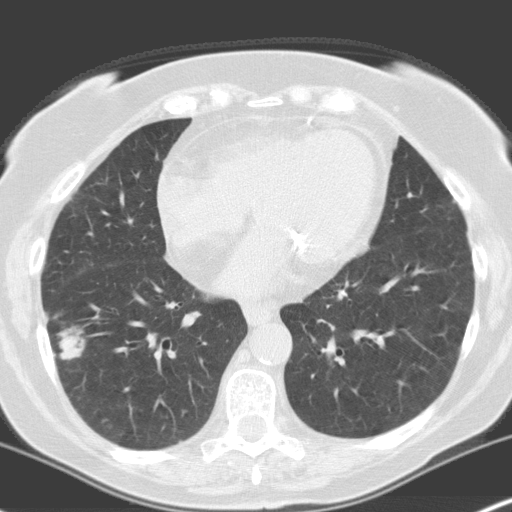
Low-dose screening chest CT, one axial slice; 120 kVp; lung window (W 1500 / L -600 HU); 3.2 mm slice thickness; 512 × 512 image matrix.
Annotated regions visible in this slice (outlined manually by an expert reader):
- lesion 1 (tumor, lower lobe of right lung): bounding box [x1, y1, x2, y2] px = [59, 327, 85, 360]